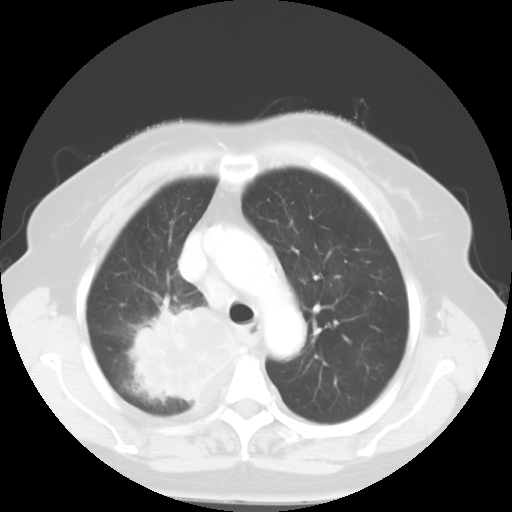
Chest CT, one axial slice. Position 39 of 52 along the scan axis. 120 kVp. Lung window (W 1500 / L -600 HU). 5 mm slice thickness. 512 × 512 image matrix, field of view 333 × 333 mm. Patient: female, 81 years. Case-level facts recorded for this patient, not image findings: clinical TNM (as recorded): T4 N3 M1b.
Structures marked on this image (rectangle marked by the reading radiologist):
- lung tumour (recorded histology: adenocarcinoma): box from (x=131, y=295) to (x=242, y=405) px